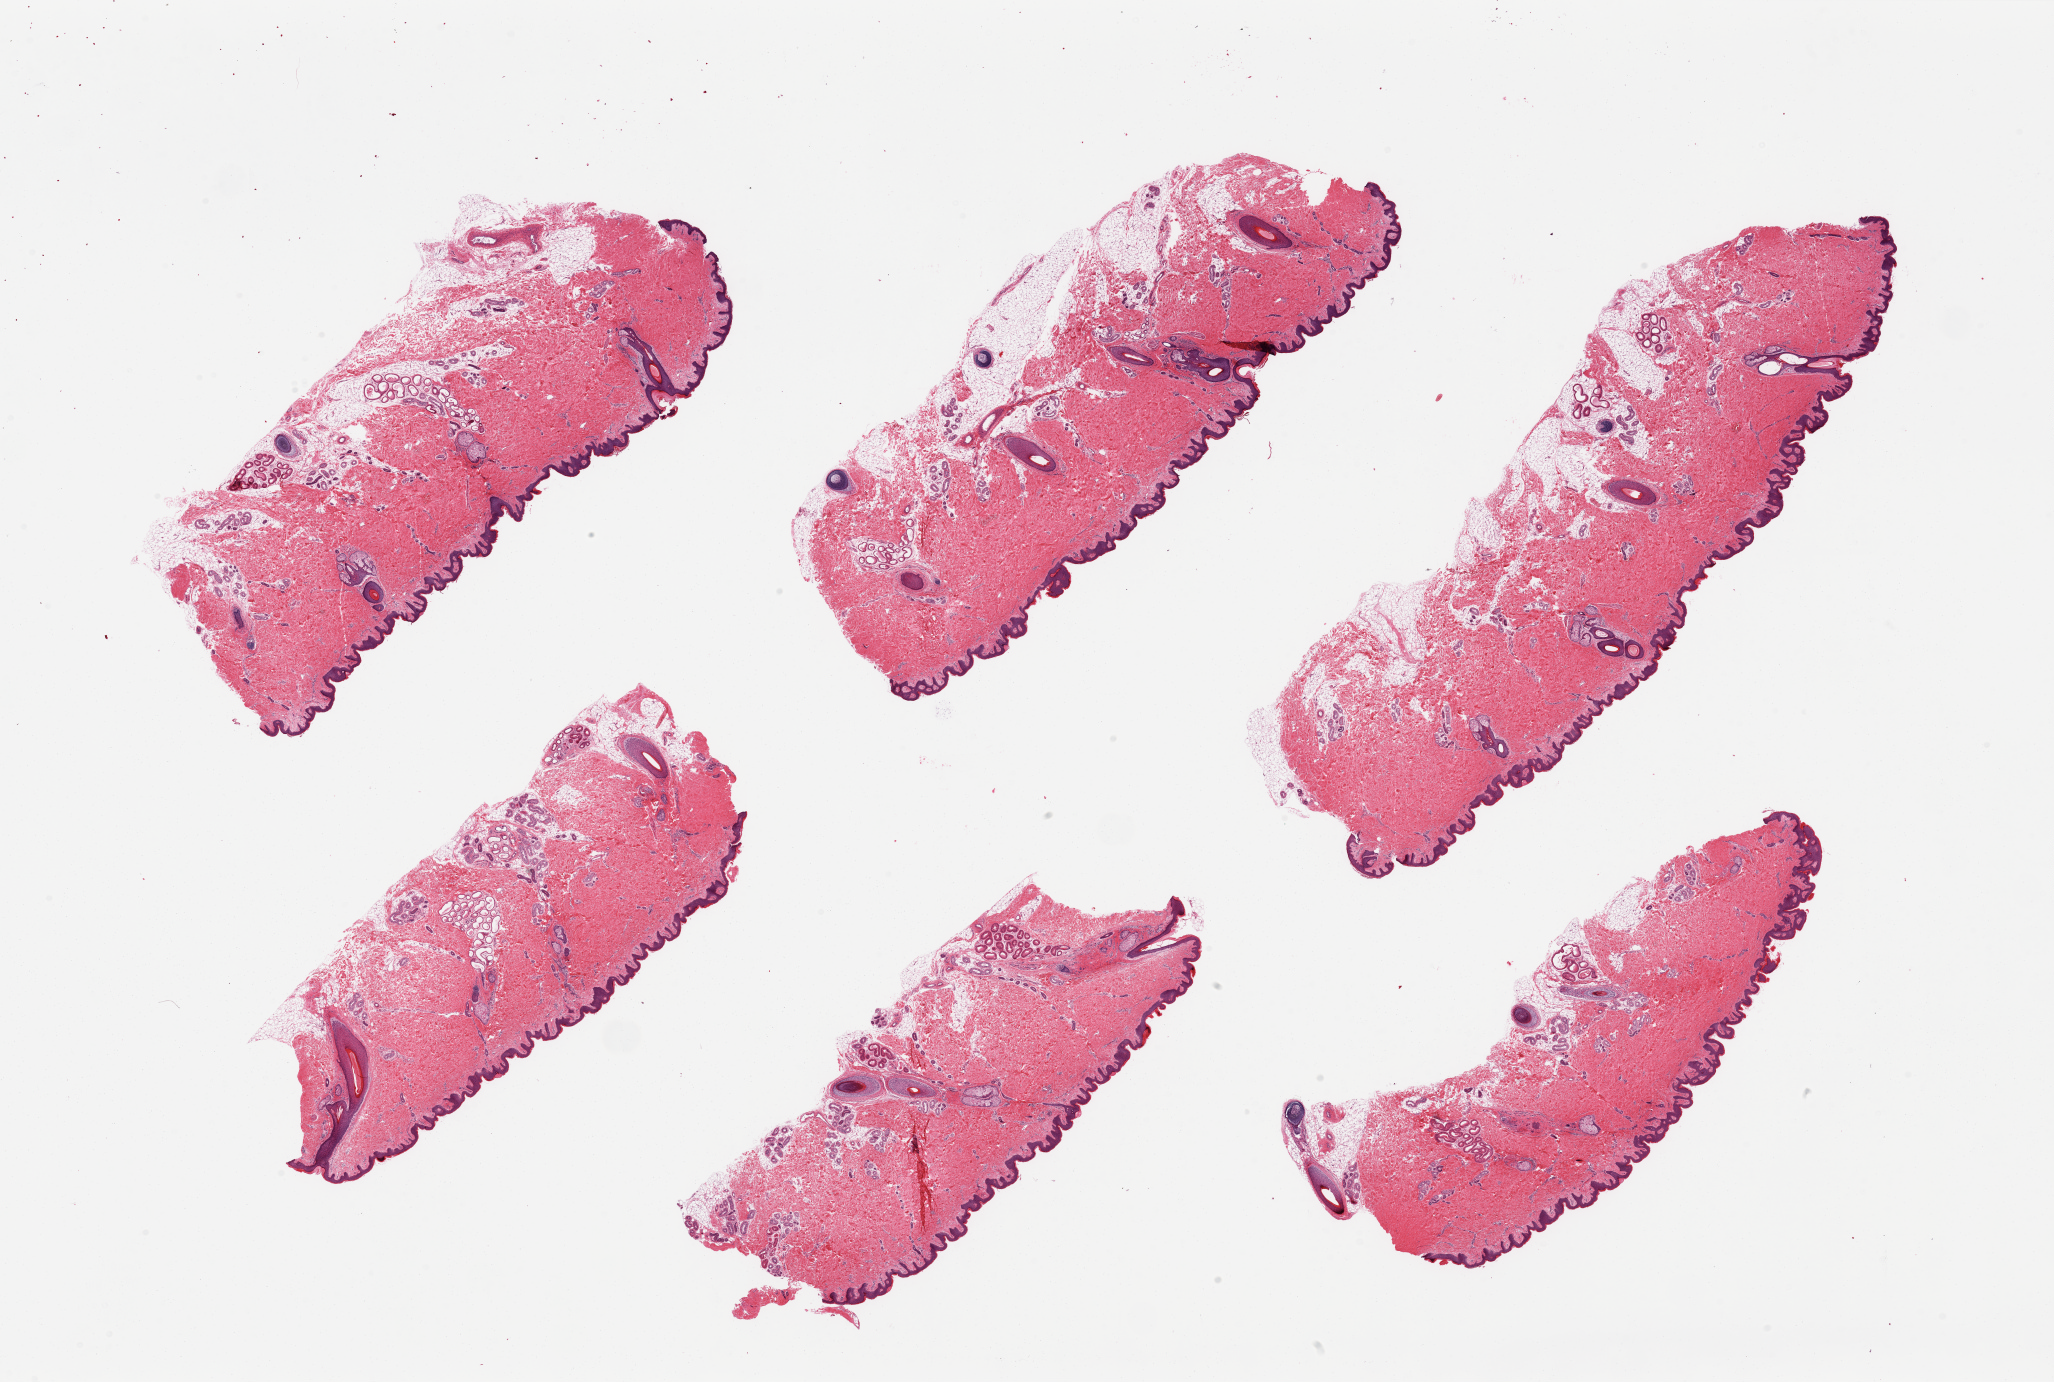
Digitized hematoxylin and eosin (H&E)-stained section, brightfield, low-resolution overview of the scanned area, about 32.5 x 21.9 mm, PAXgene-fixed, paraffin-embedded tissue, section of skin of suprapubic region (target tissue), donor tissue sample. Donor sex: male.
- reviewer comment on this tissue sample: 6 pieces, several include attached and internal fat up to 20%, numerous hair follicles, sweat and sebaceous glands